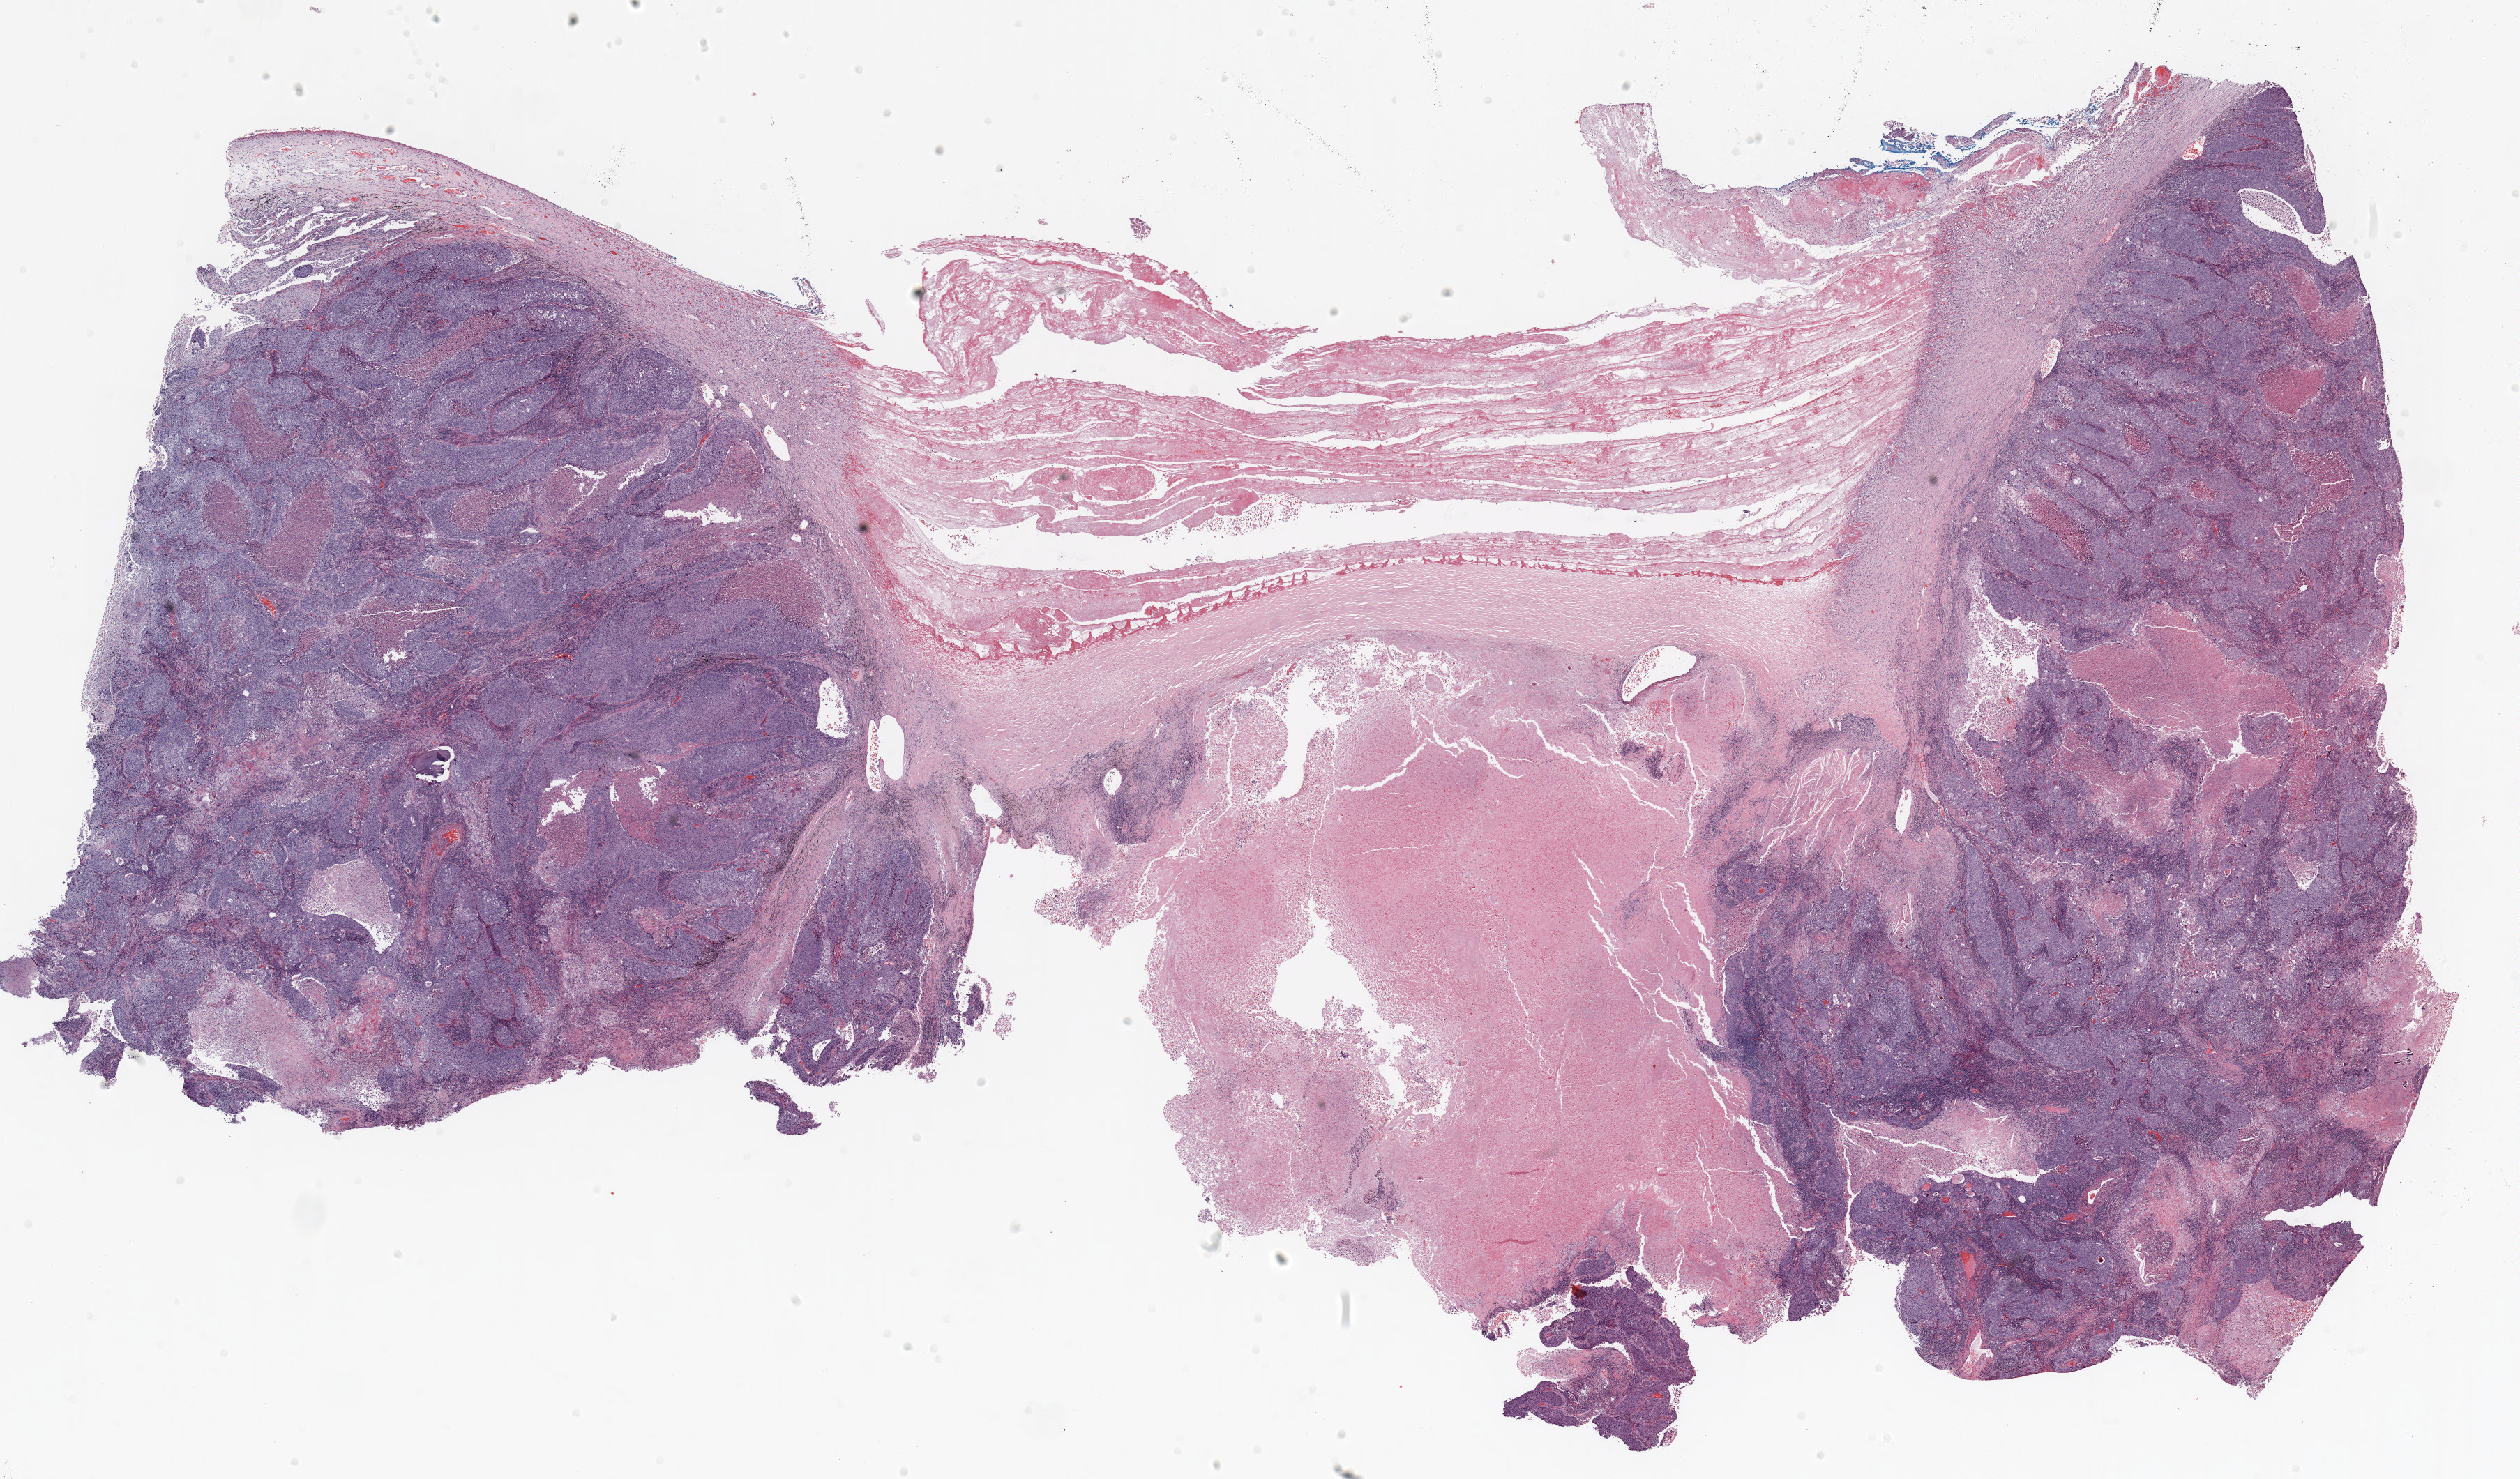
Hematoxylin and eosin (H&E) stained whole-slide image, low-resolution overview of the scanned area, about 29.0 x 17.0 mm. Formalin-fixed paraffin-embedded (FFPE) section. Lung. Male patient, aged 72 at enrolment. Current smoker at enrolment. Grade: poorly differentiated (G3).
Primary tumour location (clinical record): left lower lobe. Stage (AJCC 6th edition): IB. Tumour size (pathology): 100 mm. Participant's lung-cancer diagnosis: Large cell carcinoma, NOS (ICD-O-3 8012/3).